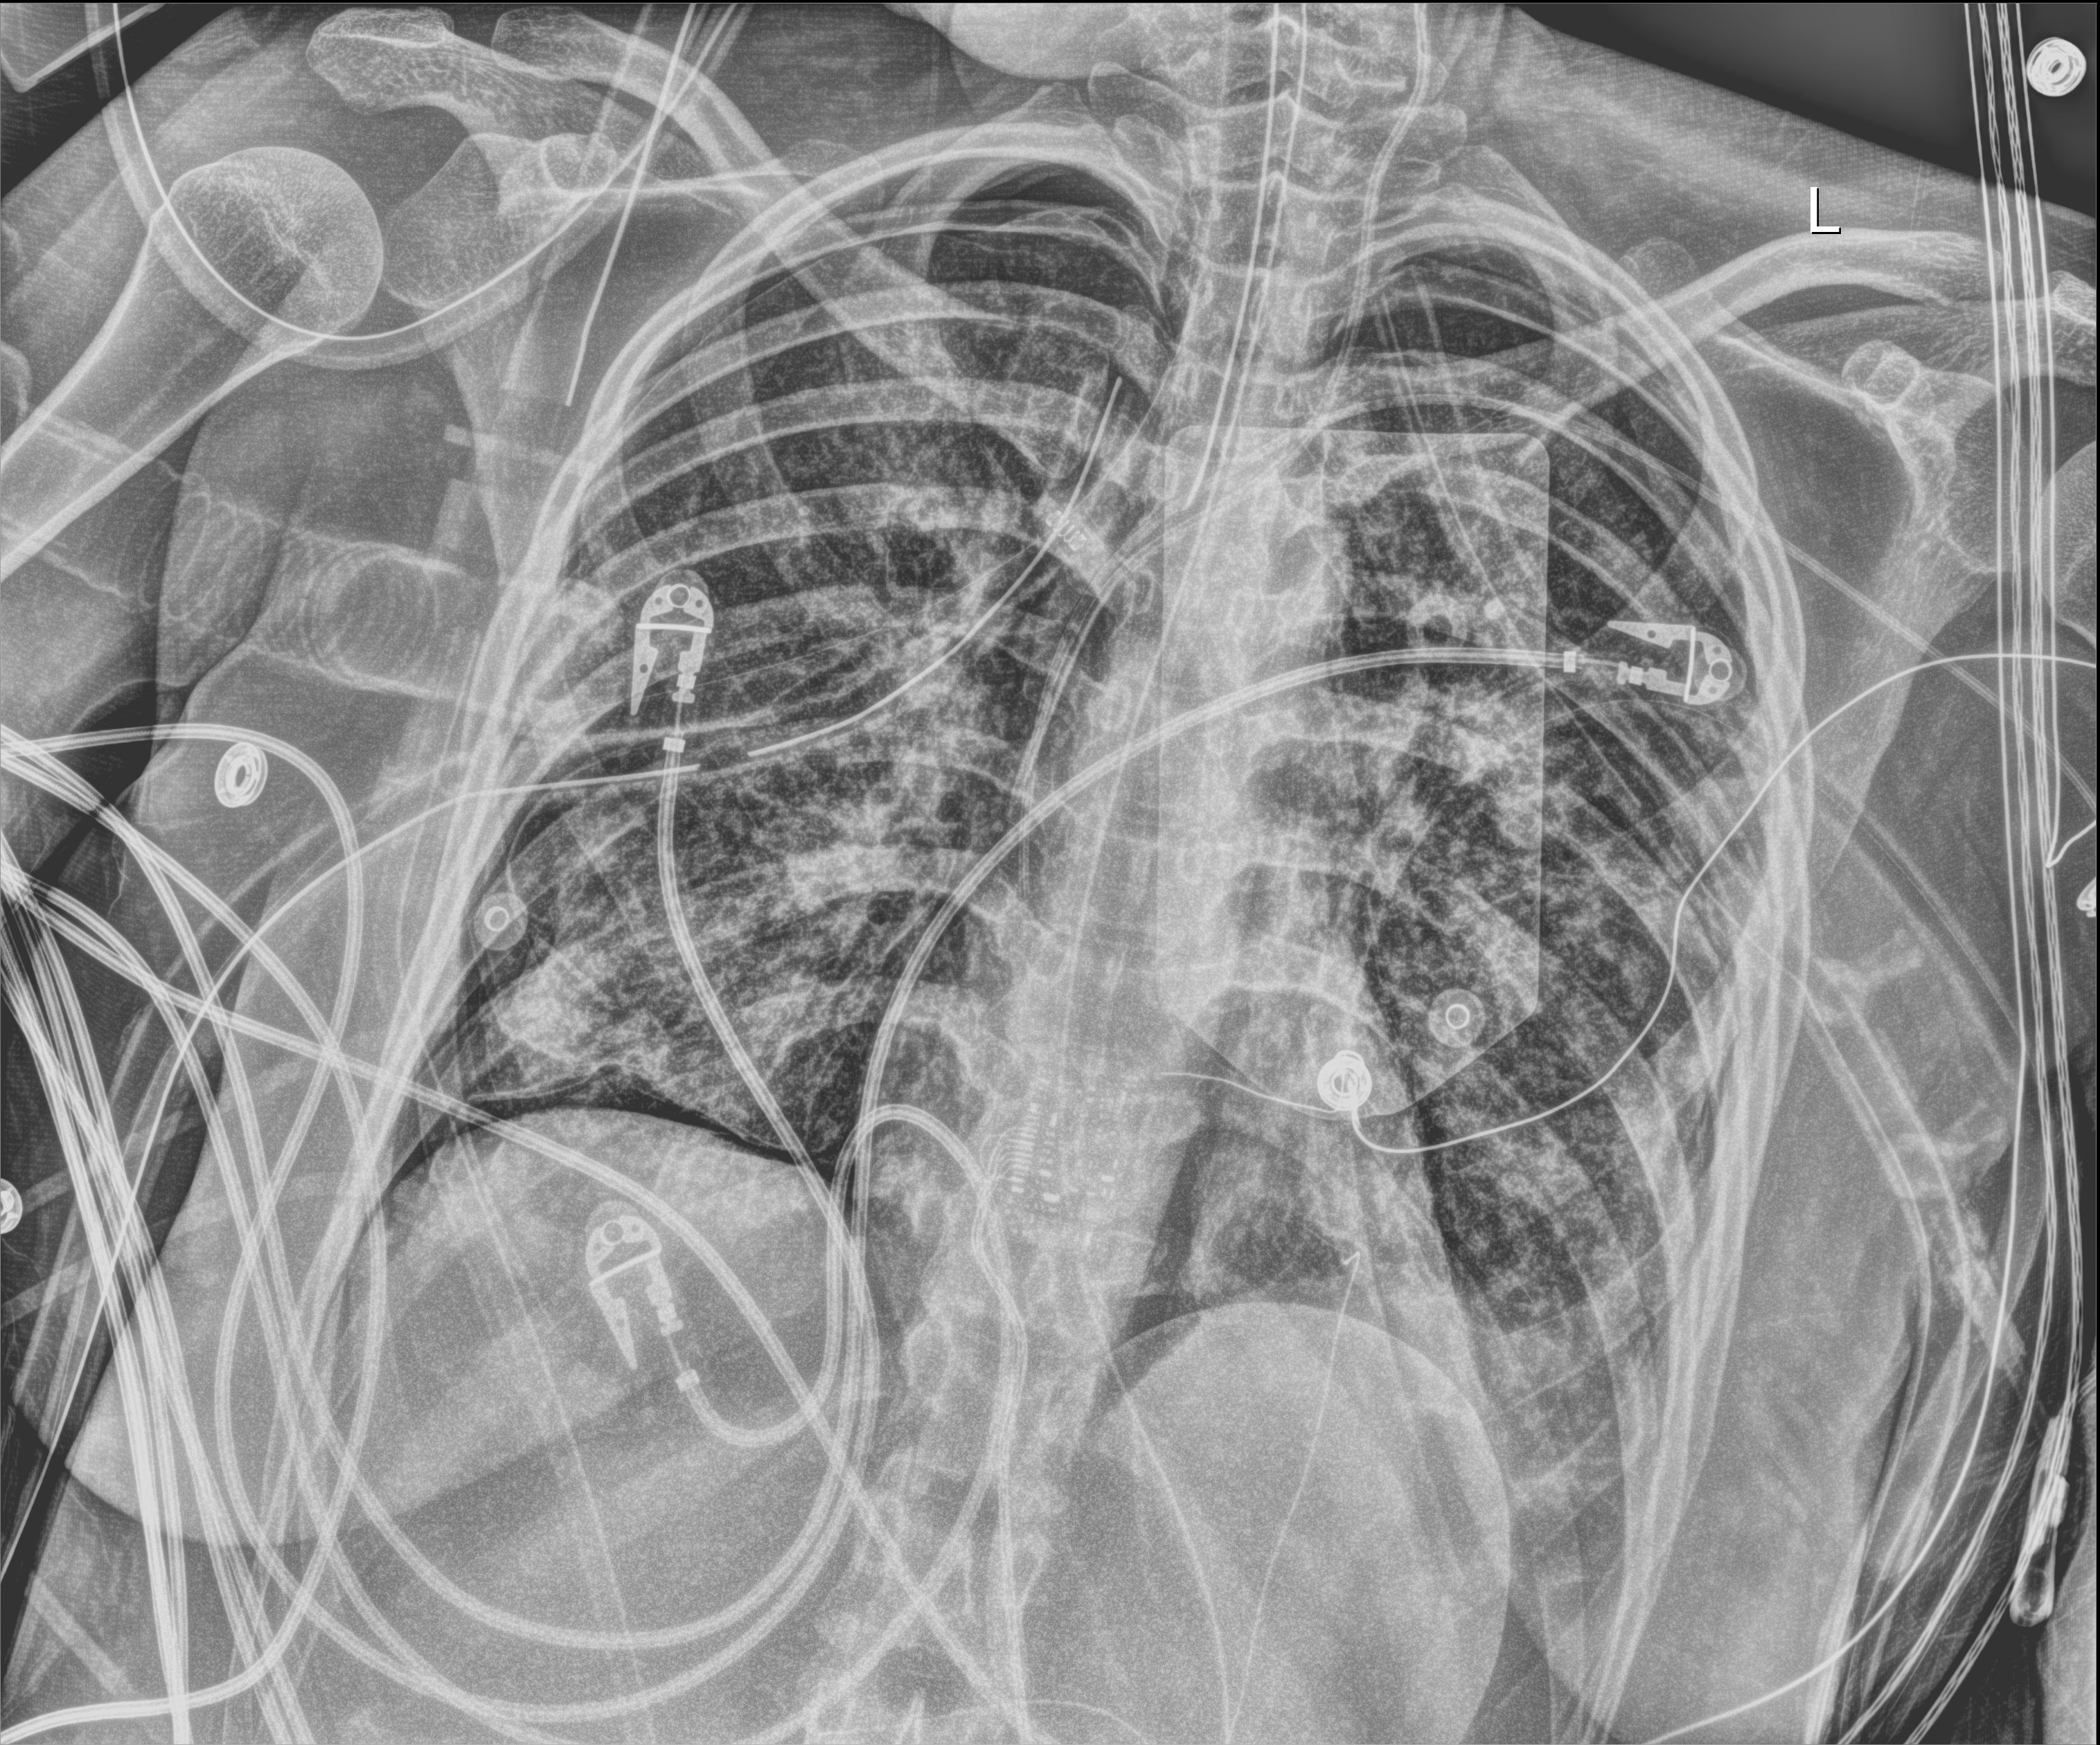
Chest X-ray (portable), anteroposterior (AP) projection. Adult patient hospitalised with COVID-19, age 18–59 years.
From the hospital-stay record, not from the radiograph (when in the stay this image was taken is not recorded): hypertension (admission record): no; admitted to intensive care during this hospital stay: yes.